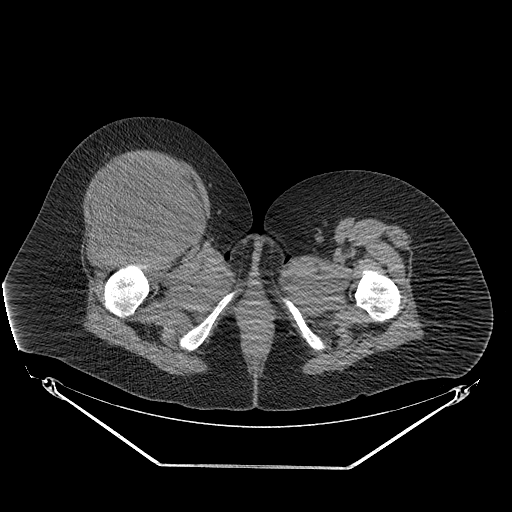
CT of an extremity soft-tissue mass (from a PET/CT study), one axial slice. Position 53 of 267 along the scan axis. Reconstruction kernel STANDARD. Soft-tissue window (W 400 / L 40 HU). 3.75 mm slice thickness. 512 × 512 image matrix, field of view 500 × 500 mm. Female patient. Case-level facts recorded for this patient, not image findings: histological type: malignant solitary fibrous tumor; grade: intermediate; site of the primary tumour: right thigh.
Outlined on this slice (expert contour drawn on MRI and transferred to this co-registered scan by the dataset authors):
- gross tumour volume including surrounding oedema: box from (x=78, y=158) to (x=200, y=243) px
- gross tumour volume (mass): (x=80, y=160)–(x=195, y=243)